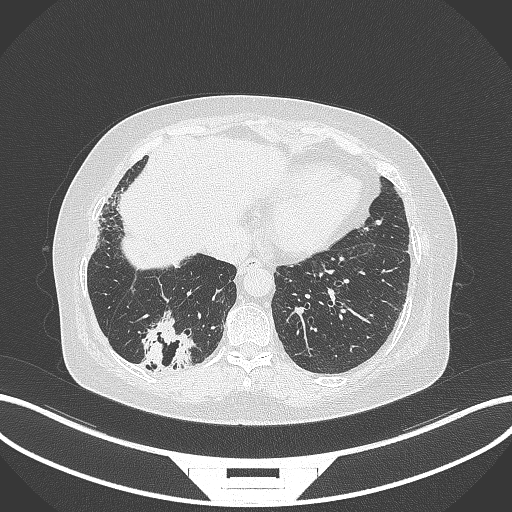
Chest CT, one axial slice; slice 50 of 296 in the series (ordered by position); reconstruction kernel B70f; 120 kVp; lung window (W 1500 / L -600 HU); 1 mm slice thickness; 512 × 512 image matrix, field of view 400 × 400 mm. Female patient, age 65 years. Case-level facts recorded for this patient, not image findings: clinical TNM (as recorded): T2b N1 M0.
Annotated regions visible in this slice (bounding box drawn by a radiologist):
- lung tumour (recorded histology: adenocarcinoma): bounding box <138,310,195,371> (left, top, right, bottom; pixels)